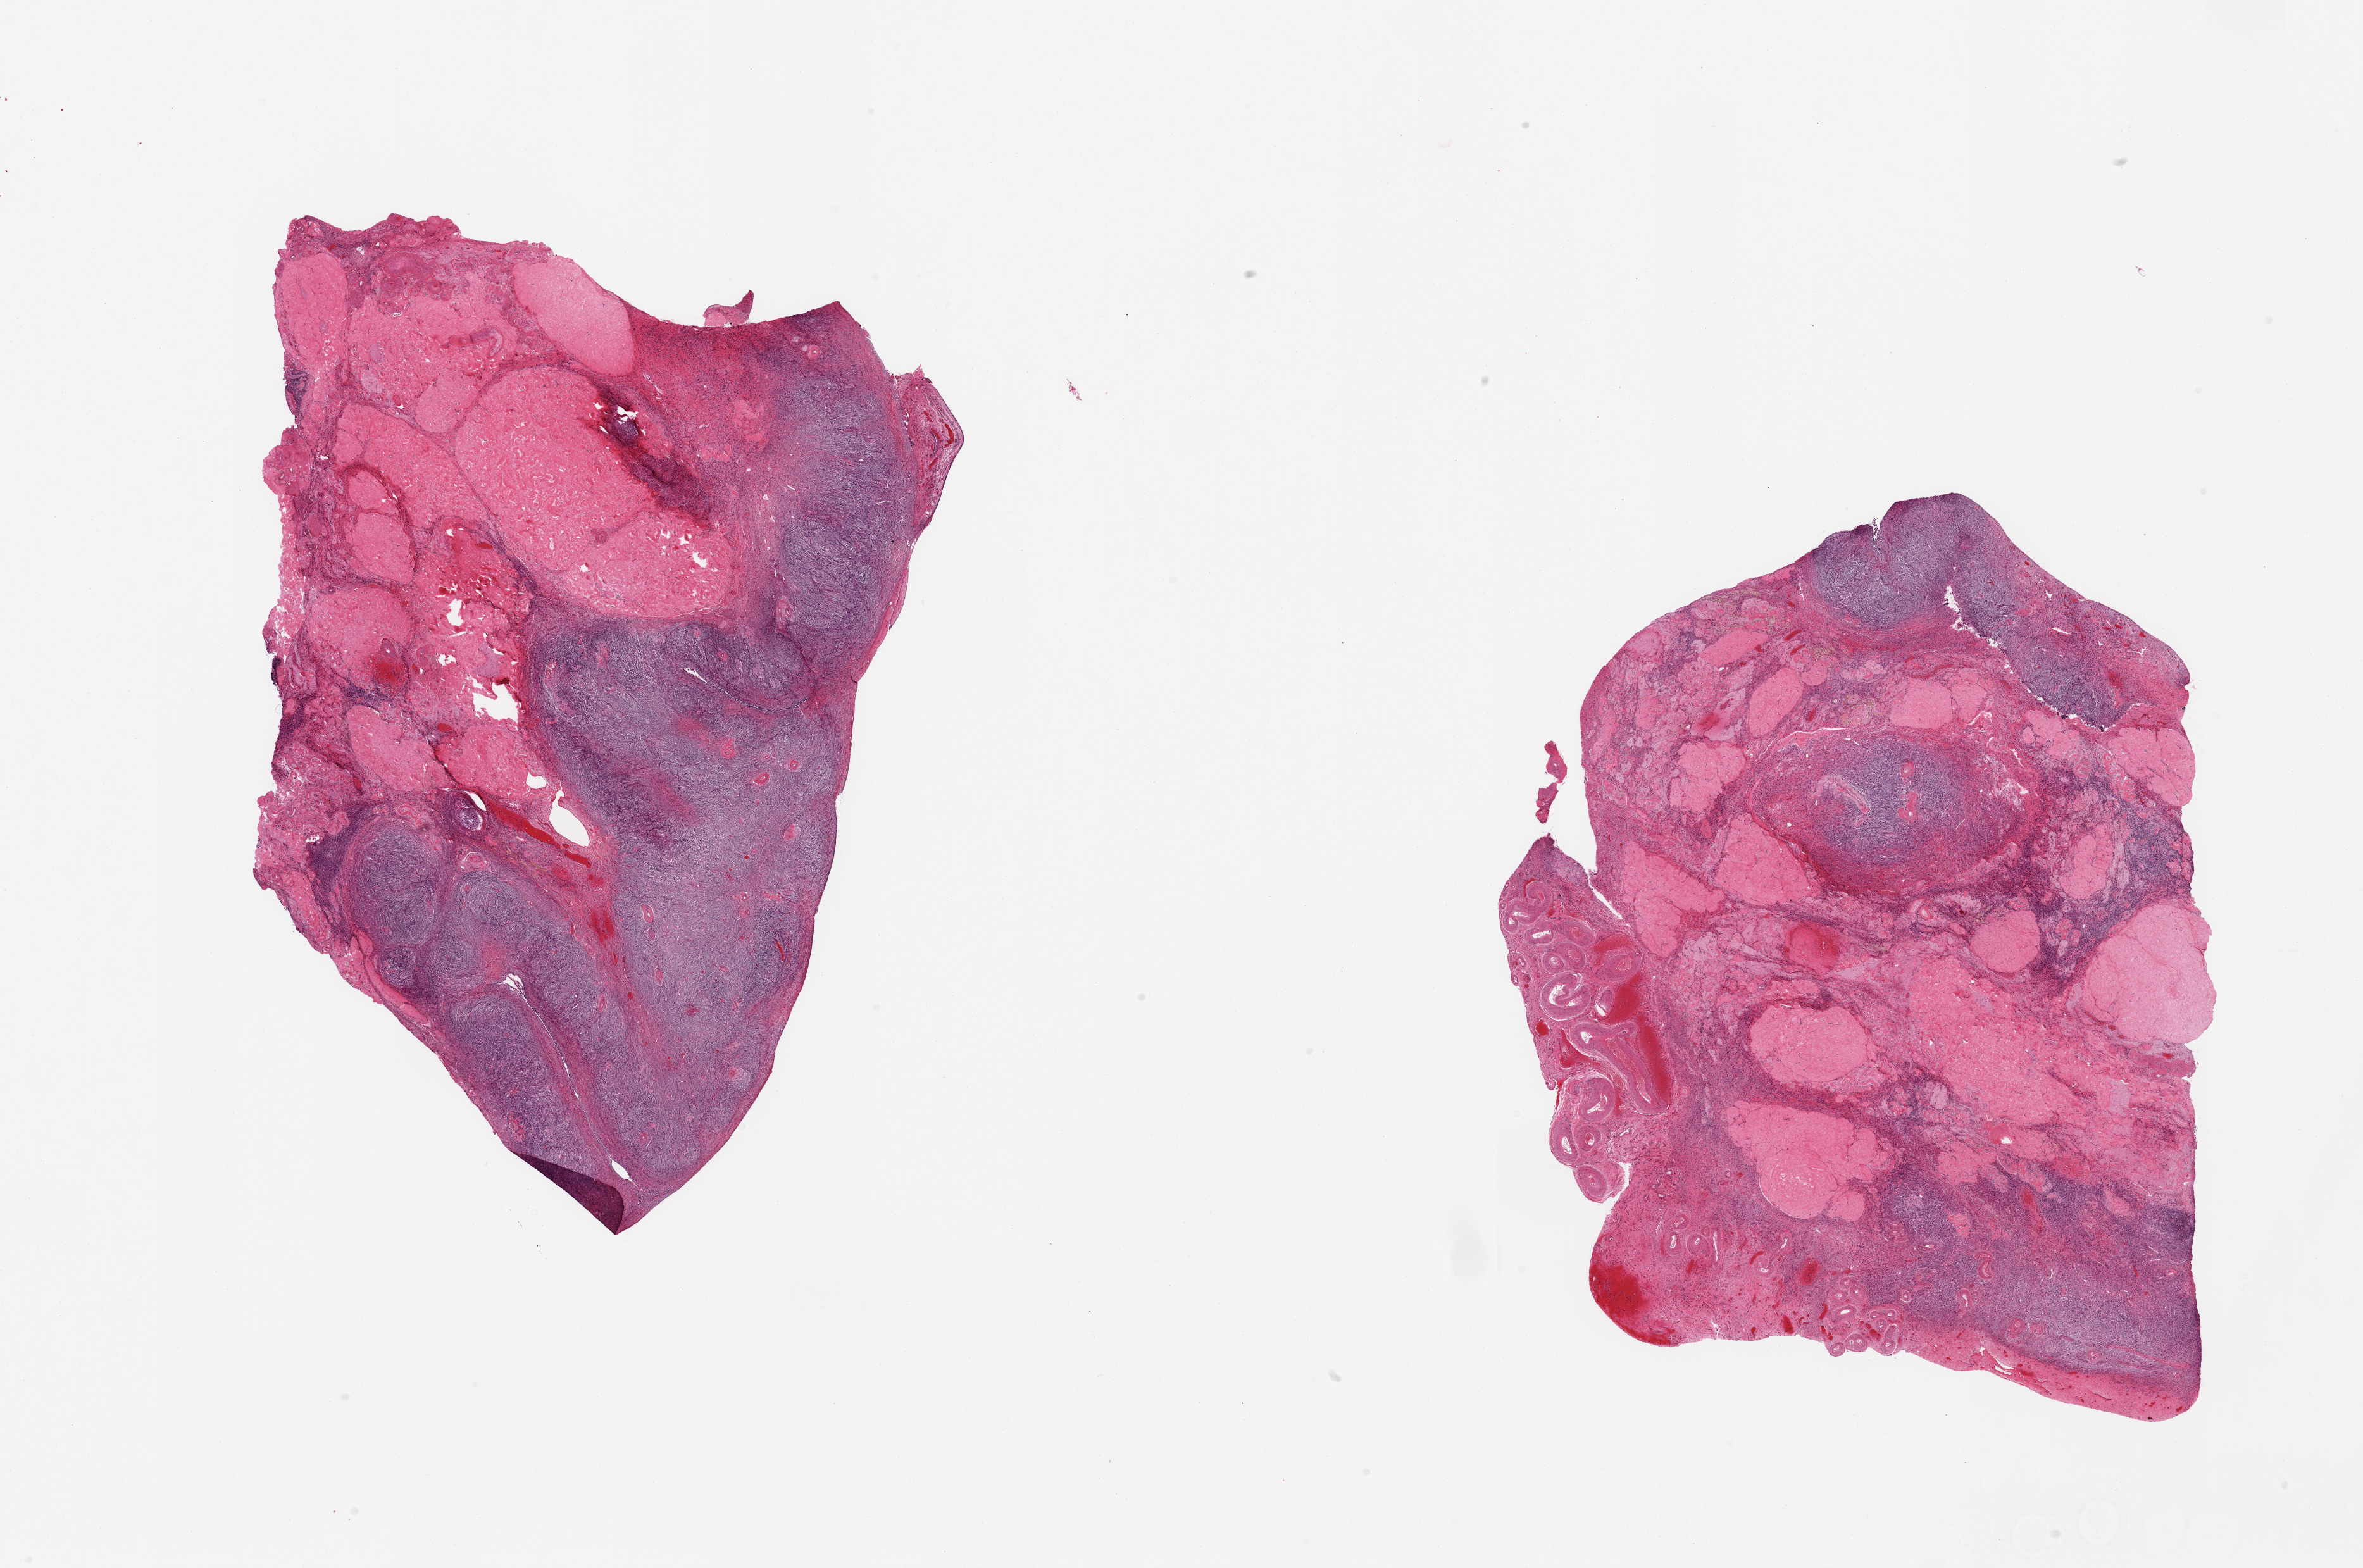
Digitized hematoxylin and eosin (H&E)-stained section, whole scanned area (about 29.5 x 19.6 mm) shown as a low-resolution overview. PAXgene-fixed paraffin-embedded (PFPE) section. Section of ovary (target tissue). Tissue donor sample.
Review note (as recorded): 2 pieces, post menopausal cortical atrophy.